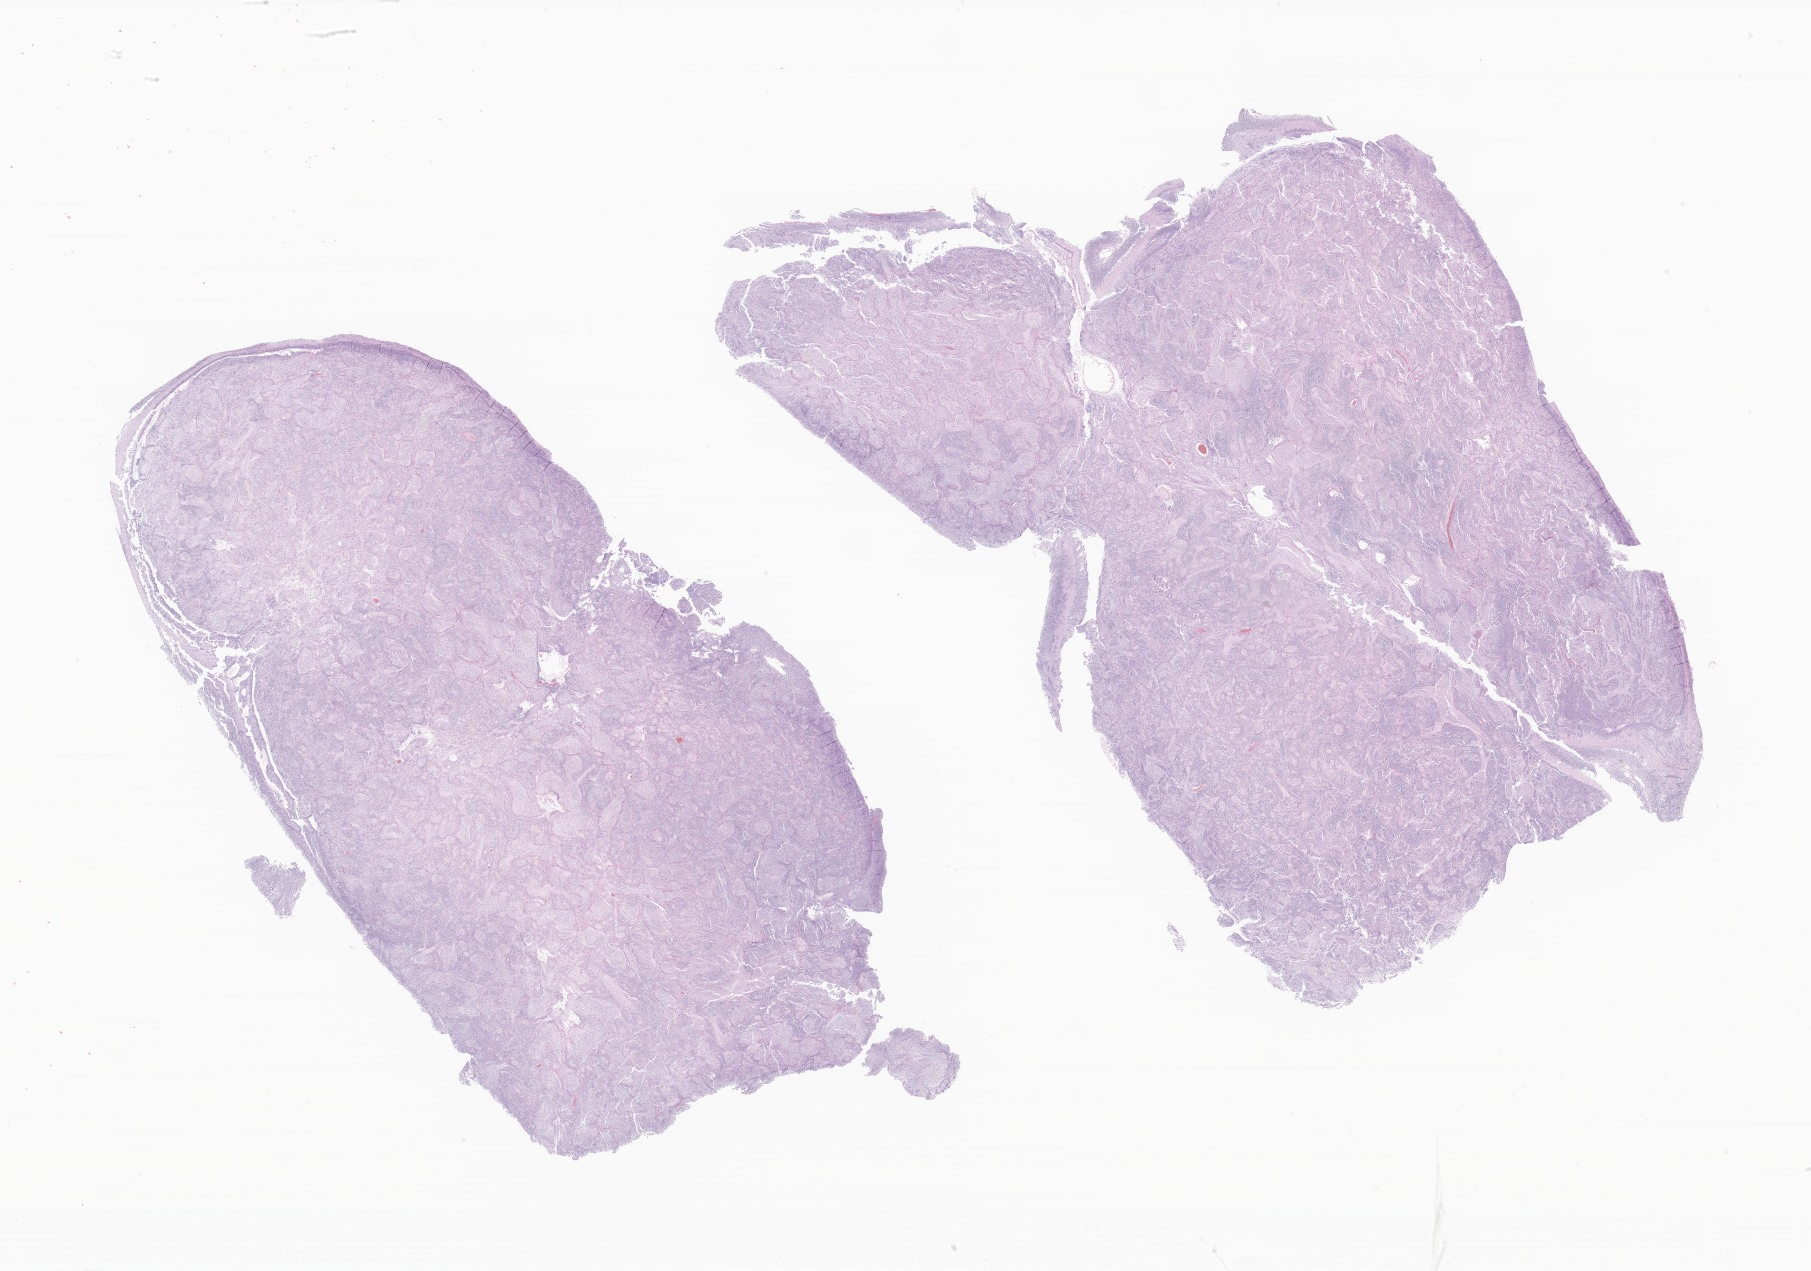
Hematoxylin and eosin (H&E) whole-slide image of tumor tissue from the brain, whole scanned area (about 30.6 x 21.4 mm) shown as a low-resolution overview; formalin-fixed paraffin-embedded section. Male patient, age 312 days.
Diagnosis (ICD-O-3 morphology term): Medulloblastoma, NOS.